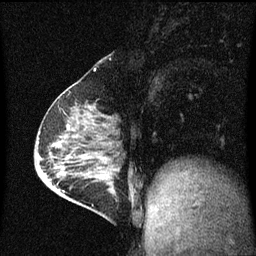
Breast MRI (dynamic contrast-enhanced), one sagittal slice; position 25 of 60 along the scan axis; dynamic contrast-enhanced series, image 2 of 3 at this slice position (ordered by acquisition); 1.5 T; TE 4.2 ms, TR 8 ms; 256 × 256 image matrix, field of view 200 × 200 mm. Patient: female, 64 years.
Structures marked on this image (semi-automatically segmented with operator editing):
- analysis volume of interest (the breast-tissue region the enhancement analysis was run in; not a lesion): bounding box [x1, y1, x2, y2] px = [87, 176, 130, 217]
- tumour enhancement mask (voxels above the 70 % enhancement threshold inside the analysis volume of interest): [91, 176, 113, 187]